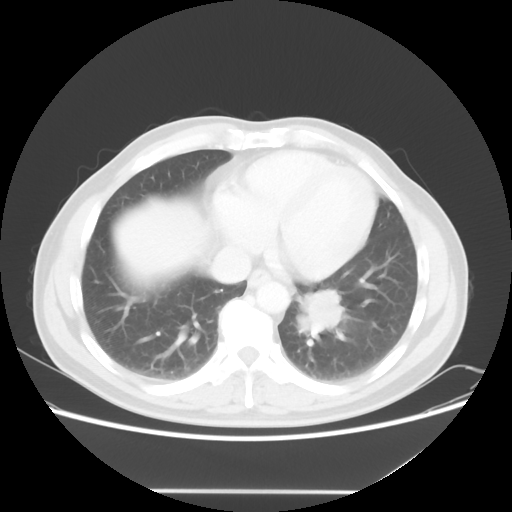
Chest CT, one axial slice; position 18 of 56 along the scan axis; reconstruction kernel STANDARD; 120 kVp; lung window (W 1500 / L -600 HU); 512 × 512 image matrix. Patient: male, 61 years. Case-level facts recorded for this patient, not image findings: clinical TNM (as recorded): T1c N0 M0; histopathological grade: G3.
Annotated regions visible in this slice (rectangle marked by the reading radiologist):
- lung tumour (recorded histology: adenocarcinoma): bounding box <292,283,353,339> (left, top, right, bottom; pixels)